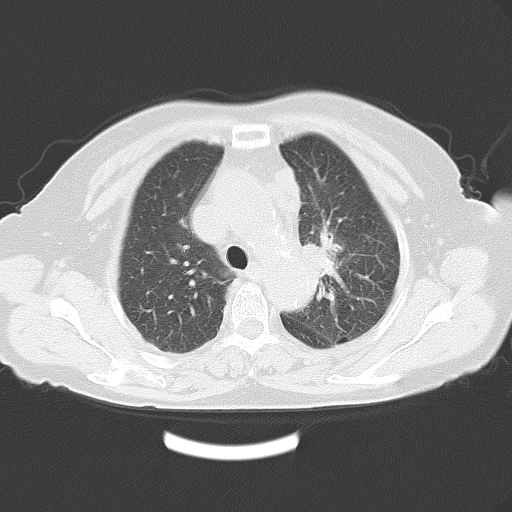
Chest CT, one axial slice; position 40 of 54 along the scan axis; lung window (W 1500 / L -600 HU); 512 × 512 image matrix, field of view 353 × 353 mm. Patient: female, 71 years. Case-level facts recorded for this patient, not image findings: clinical TNM (as recorded): T3 N3 M0.
Annotated regions visible in this slice (bounding box drawn by a radiologist):
- lung tumour (recorded histology: adenocarcinoma): box from (x=304, y=236) to (x=343, y=292) px